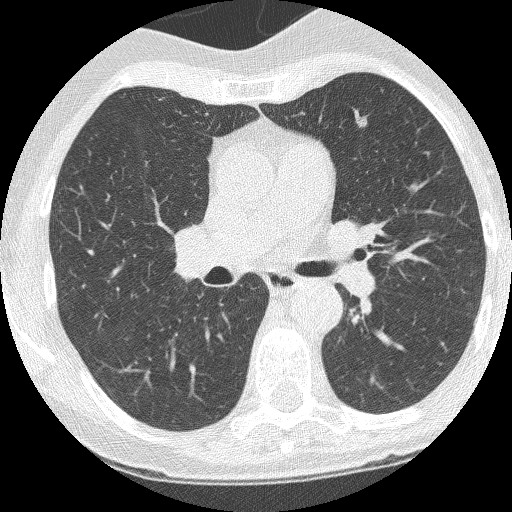
Chest CT (low-dose screening protocol), one axial image. Third screening round (two years after baseline). Lung window (W 1500 / L -600 HU). 1.25 mm slice thickness. 120 kVp. Slice 156 of 247 in the series. 512 × 512 image matrix. Female participant, aged 60 years at enrolment. Current smoker at enrolment.
Lesion marked by an expert reader, box from (x=344, y=114) to (x=376, y=142) px. The screening reader recorded 2 non-calcified nodules or masses ≥4 mm on this exam (left upper lobe, left upper lobe); which of them this box marks is not recorded. Official screen result: positive, other.